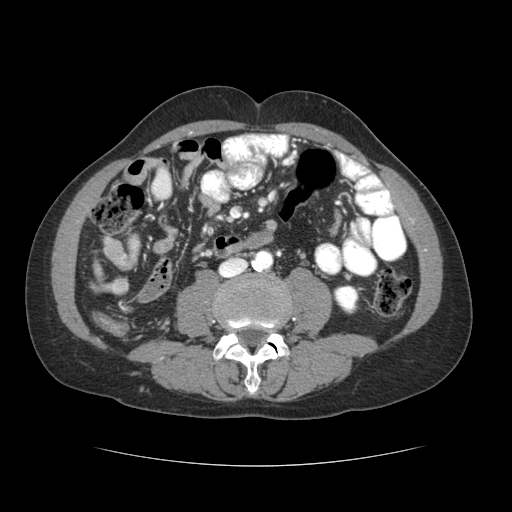
Contrast-enhanced abdominal CT (liver protocol), one axial slice. Position 3 of 69 along the scan axis. Reconstruction kernel STANDARD. 120 kVp. Soft-tissue window (W 400 / L 40 HU). 2.5 mm slice thickness. 512 × 512 image matrix, field of view 360 × 360 mm. From the clinical record (not read from this slice): diagnosis: hepatocellular carcinoma (patient treated with transarterial chemoembolisation; whether this scan precedes or follows treatment is not stated here); TNM stage (as recorded): Stage-II; Child-Pugh class: B; tumour differentiation: poorly differentiated; tumour nodularity: multinodular.
Outlined on this slice (semi-automatic segmentation, software-assisted and operator-edited):
- liver parenchyma outside the tumour (the mass and vessels are separate outlines, so this box may not span the whole liver): box from (x=94, y=260) to (x=102, y=276) px